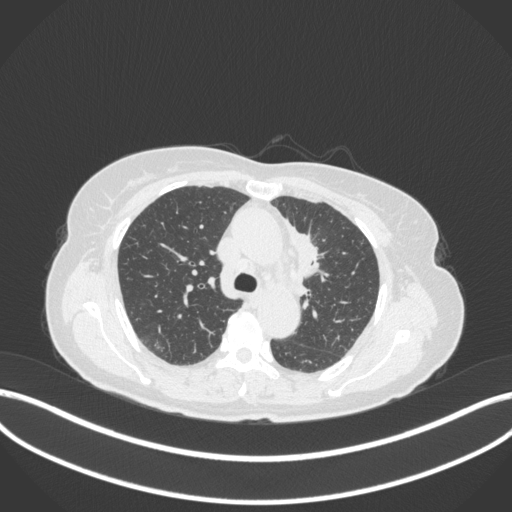
Chest CT, one axial slice; position 229 of 368 along the scan axis; reconstruction kernel B31f; 120 kVp; lung window (W 1500 / L -600 HU); 1 mm slice thickness; 512 × 512 image matrix, field of view 400 × 400 mm. Patient: female, 65 years. From the clinical record (not read from this slice): clinical TNM (as recorded): T2a N0 M0; histopathological grade: G2-3.
Annotated regions visible in this slice (rectangle marked by the reading radiologist):
- lung tumour (recorded histology: adenocarcinoma): bounding box (x1, y1, x2, y2) in pixels: (289, 227, 325, 278)